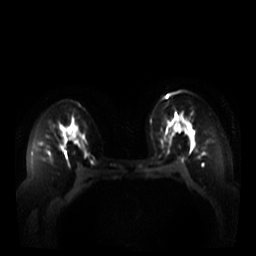
Breast MRI, one axial slice; slice 22 of 44 in the series (ordered by position); diffusion-weighted series; image 2 of 4 stored at this slice position (different b-values; order by instance number); 3 T; 5 mm slice thickness; 256 × 256 image matrix. Female patient.
Annotated regions visible in this slice (outlined manually by an expert reader):
- tumour on diffusion-weighted imaging: box from (x=188, y=130) to (x=194, y=138) px